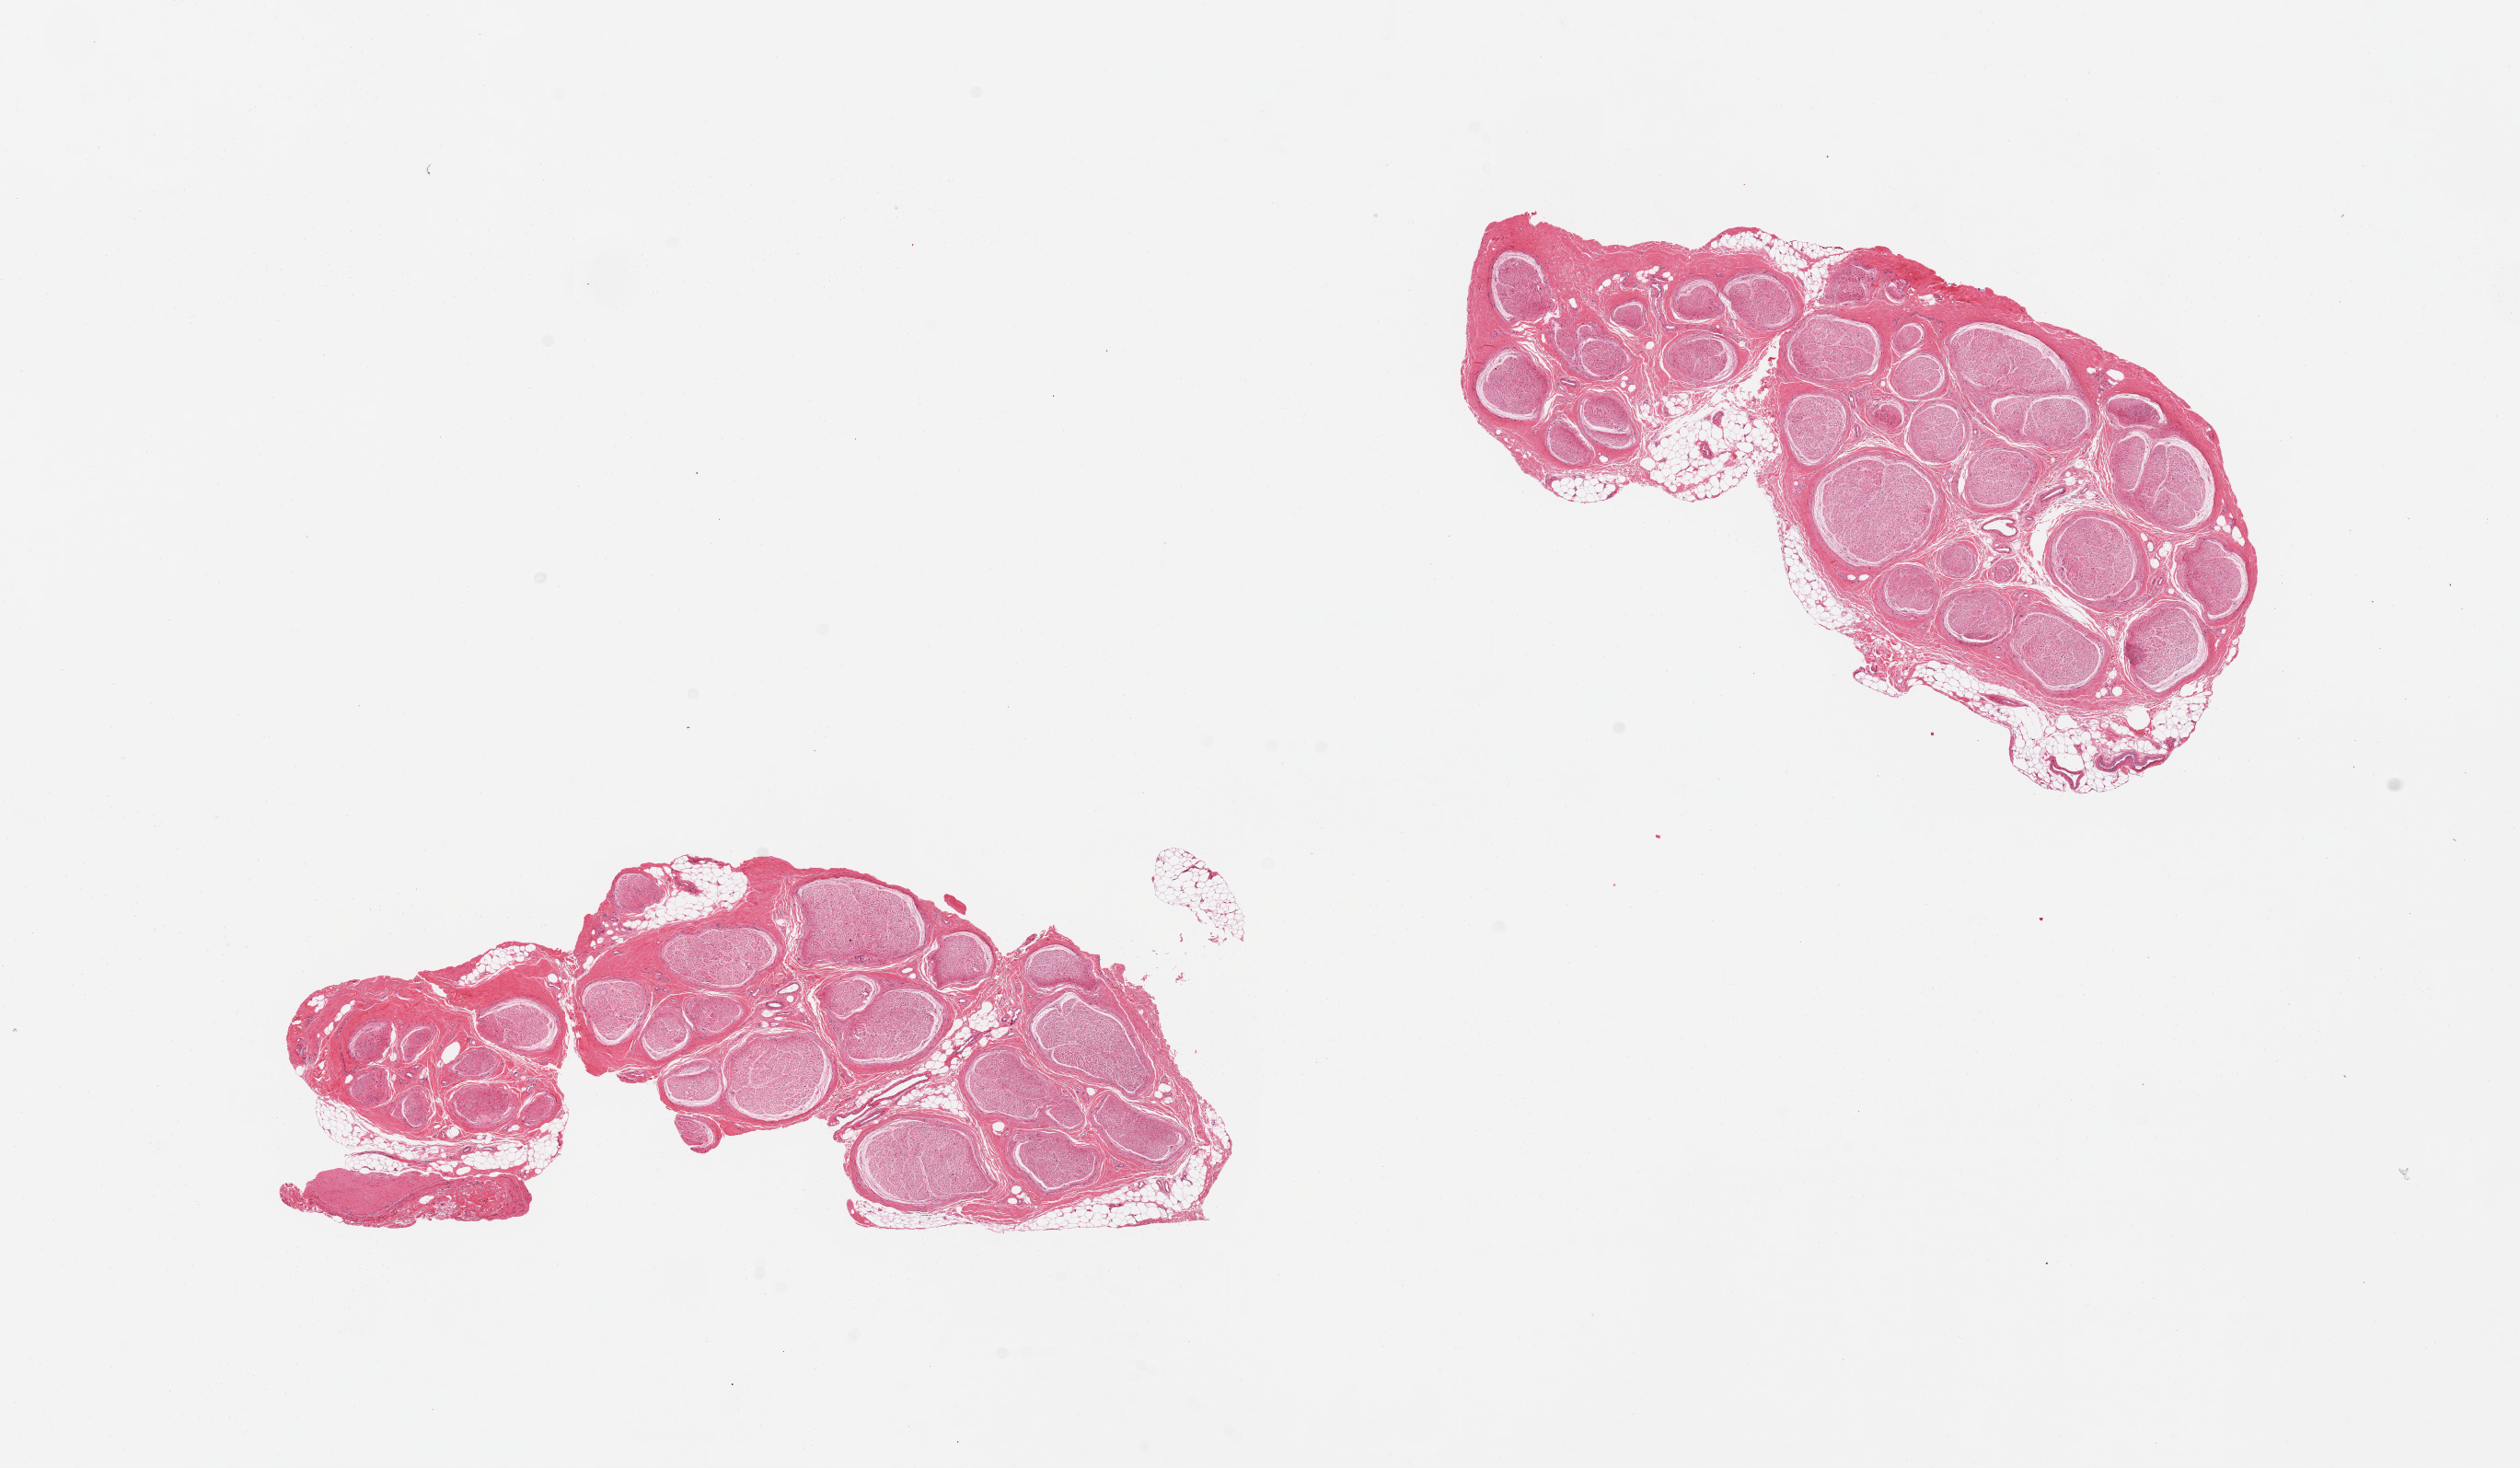
Whole-slide image, hematoxylin and eosin (H&E) stain — a low-resolution overview of the entire scanned area, about 21.7 x 12.6 mm. PAXgene-fixed paraffin-embedded (PFPE) section. Section of tibial nerve (target tissue). Donor tissue sample. Male donor.
Review note (as recorded): 2 pieces; 10% internal and external fat.